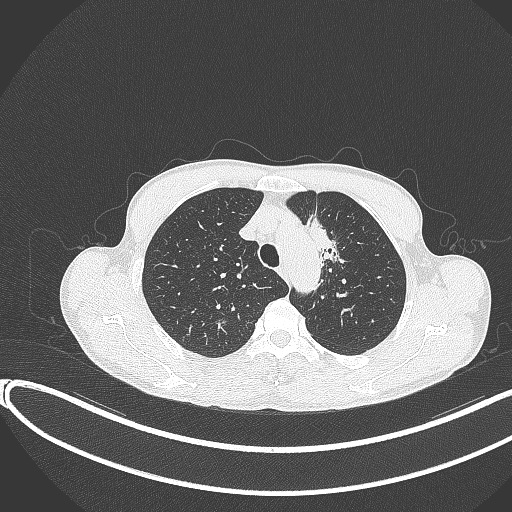
Chest CT, one axial slice. Slice 300 of 374 in the series (ordered by position). Reconstruction kernel B70f. 120 kVp. Lung window (W 1500 / L -600 HU). 512 × 512 image matrix. Male patient, age 58 years. Case-level facts recorded for this patient, not image findings: clinical TNM (as recorded): T1c N1 M0.
Annotated regions visible in this slice (rectangle marked by the reading radiologist):
- lung tumour (recorded histology: adenocarcinoma): bounding box <306,212,348,268> (left, top, right, bottom; pixels)